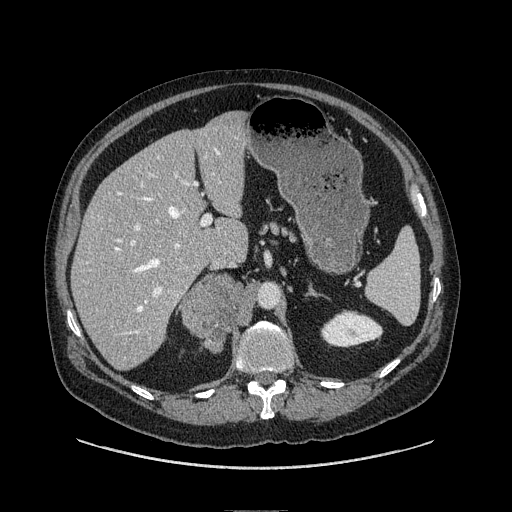
Contrast-enhanced abdominal CT, one axial slice. Position 58 of 149 along the scan axis. Soft-tissue window (W 400 / L 40 HU). 1.25 mm slice thickness. 512 × 512 image matrix. Male patient. Case-level facts recorded for this patient, not image findings: diagnosis: adrenocortical carcinoma; tumour side: right adrenal; tumour size at pathology: 7.5 cm; Ki-67 index: 15 %; stage (as recorded): 2.
Annotated regions visible in this slice (semi-automatically segmented with operator editing):
- mass: bounding box <180,270,246,352> (left, top, right, bottom; pixels)